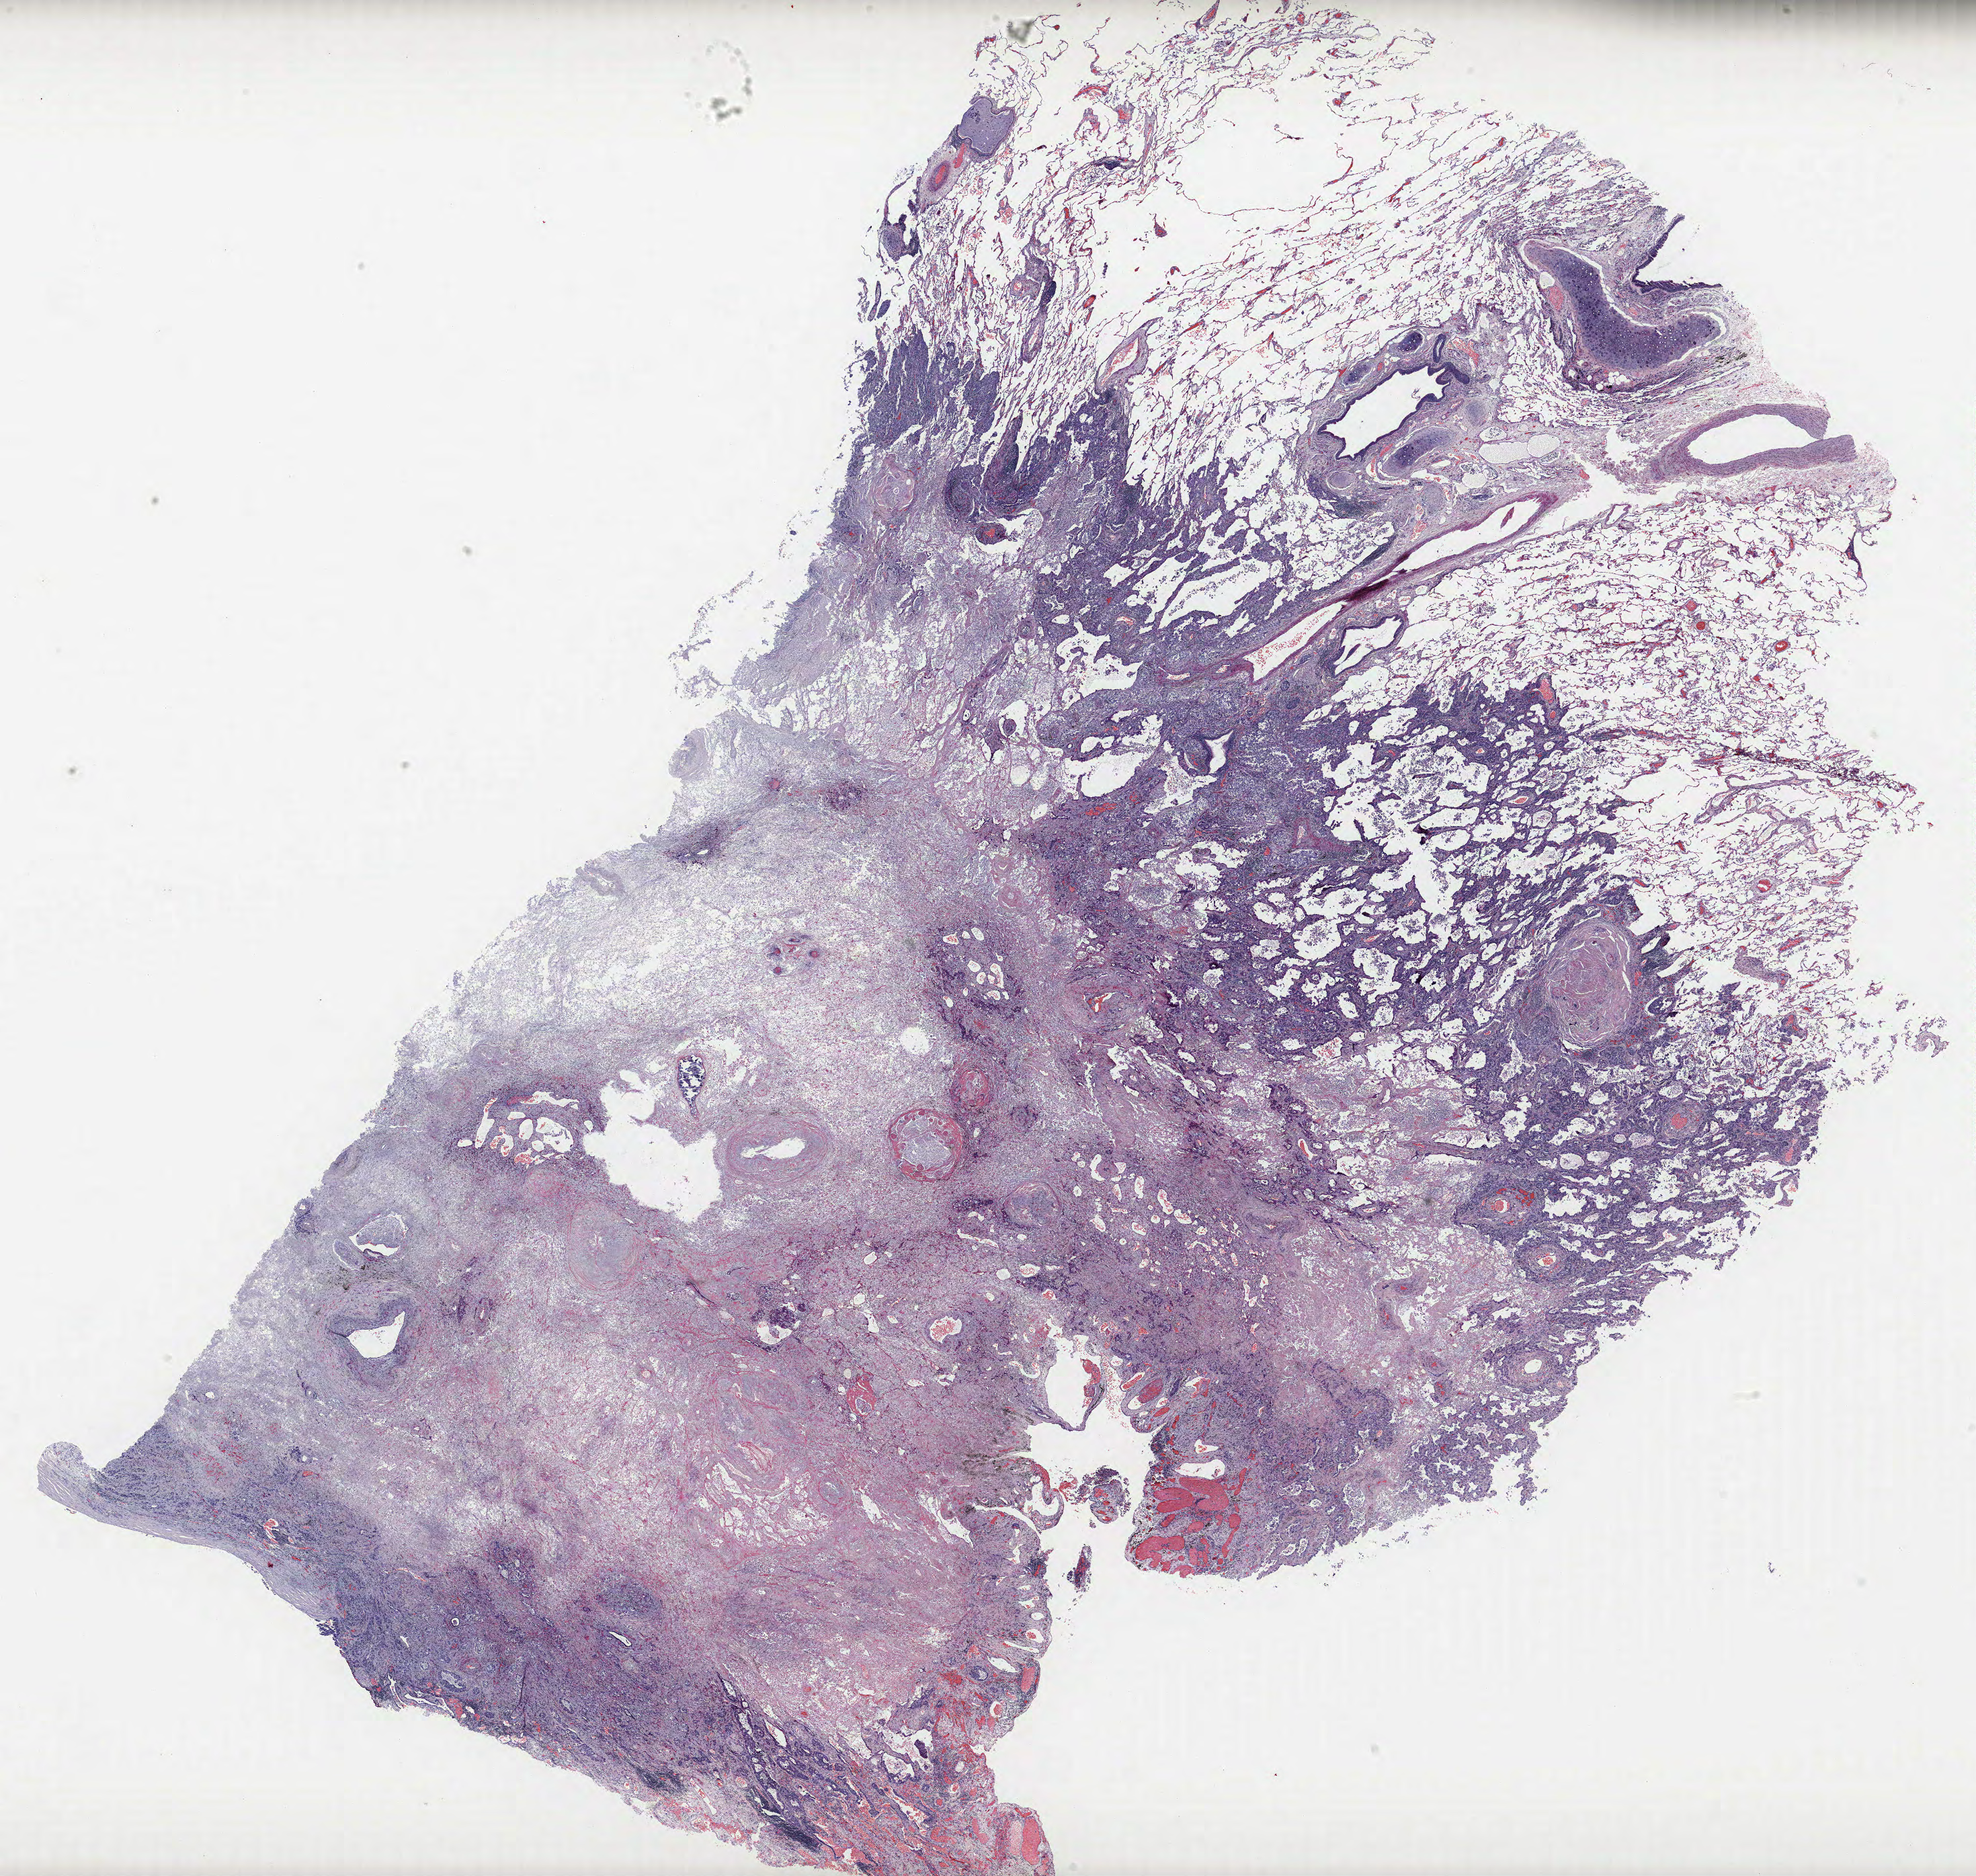
H&E whole-slide image — low-resolution overview of the scanned area, about 23.5 x 22.3 mm. FFPE section. Lung. Male patient, aged 63 at enrolment. Former smoker at enrolment. Grade: moderately differentiated (G2).
* stage (AJCC 6th edition): IIIA
* primary tumour location (clinical record): right lower lobe
* participant's lung-cancer diagnosis: Adenocarcinoma, NOS
* tumour size (pathology): 45 mm